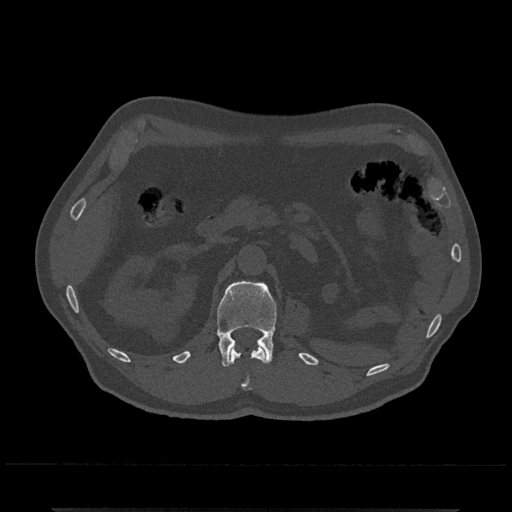
CT including the spine, one axial slice. Position 381 of 797 along the scan axis. Reconstruction kernel Br40s/3. Bone window (W 1800 / L 400 HU). 512 × 512 image matrix. Male patient, age 67 years. Case-level facts recorded for this patient, not image findings: primary cancer: prostate.
Structures marked on this image (semi-automatically segmented with operator editing):
- L1 vertebra: bounding box (x1, y1, x2, y2) in pixels: (217, 280, 277, 367)
- T12 vertebra: (230, 346, 266, 389)